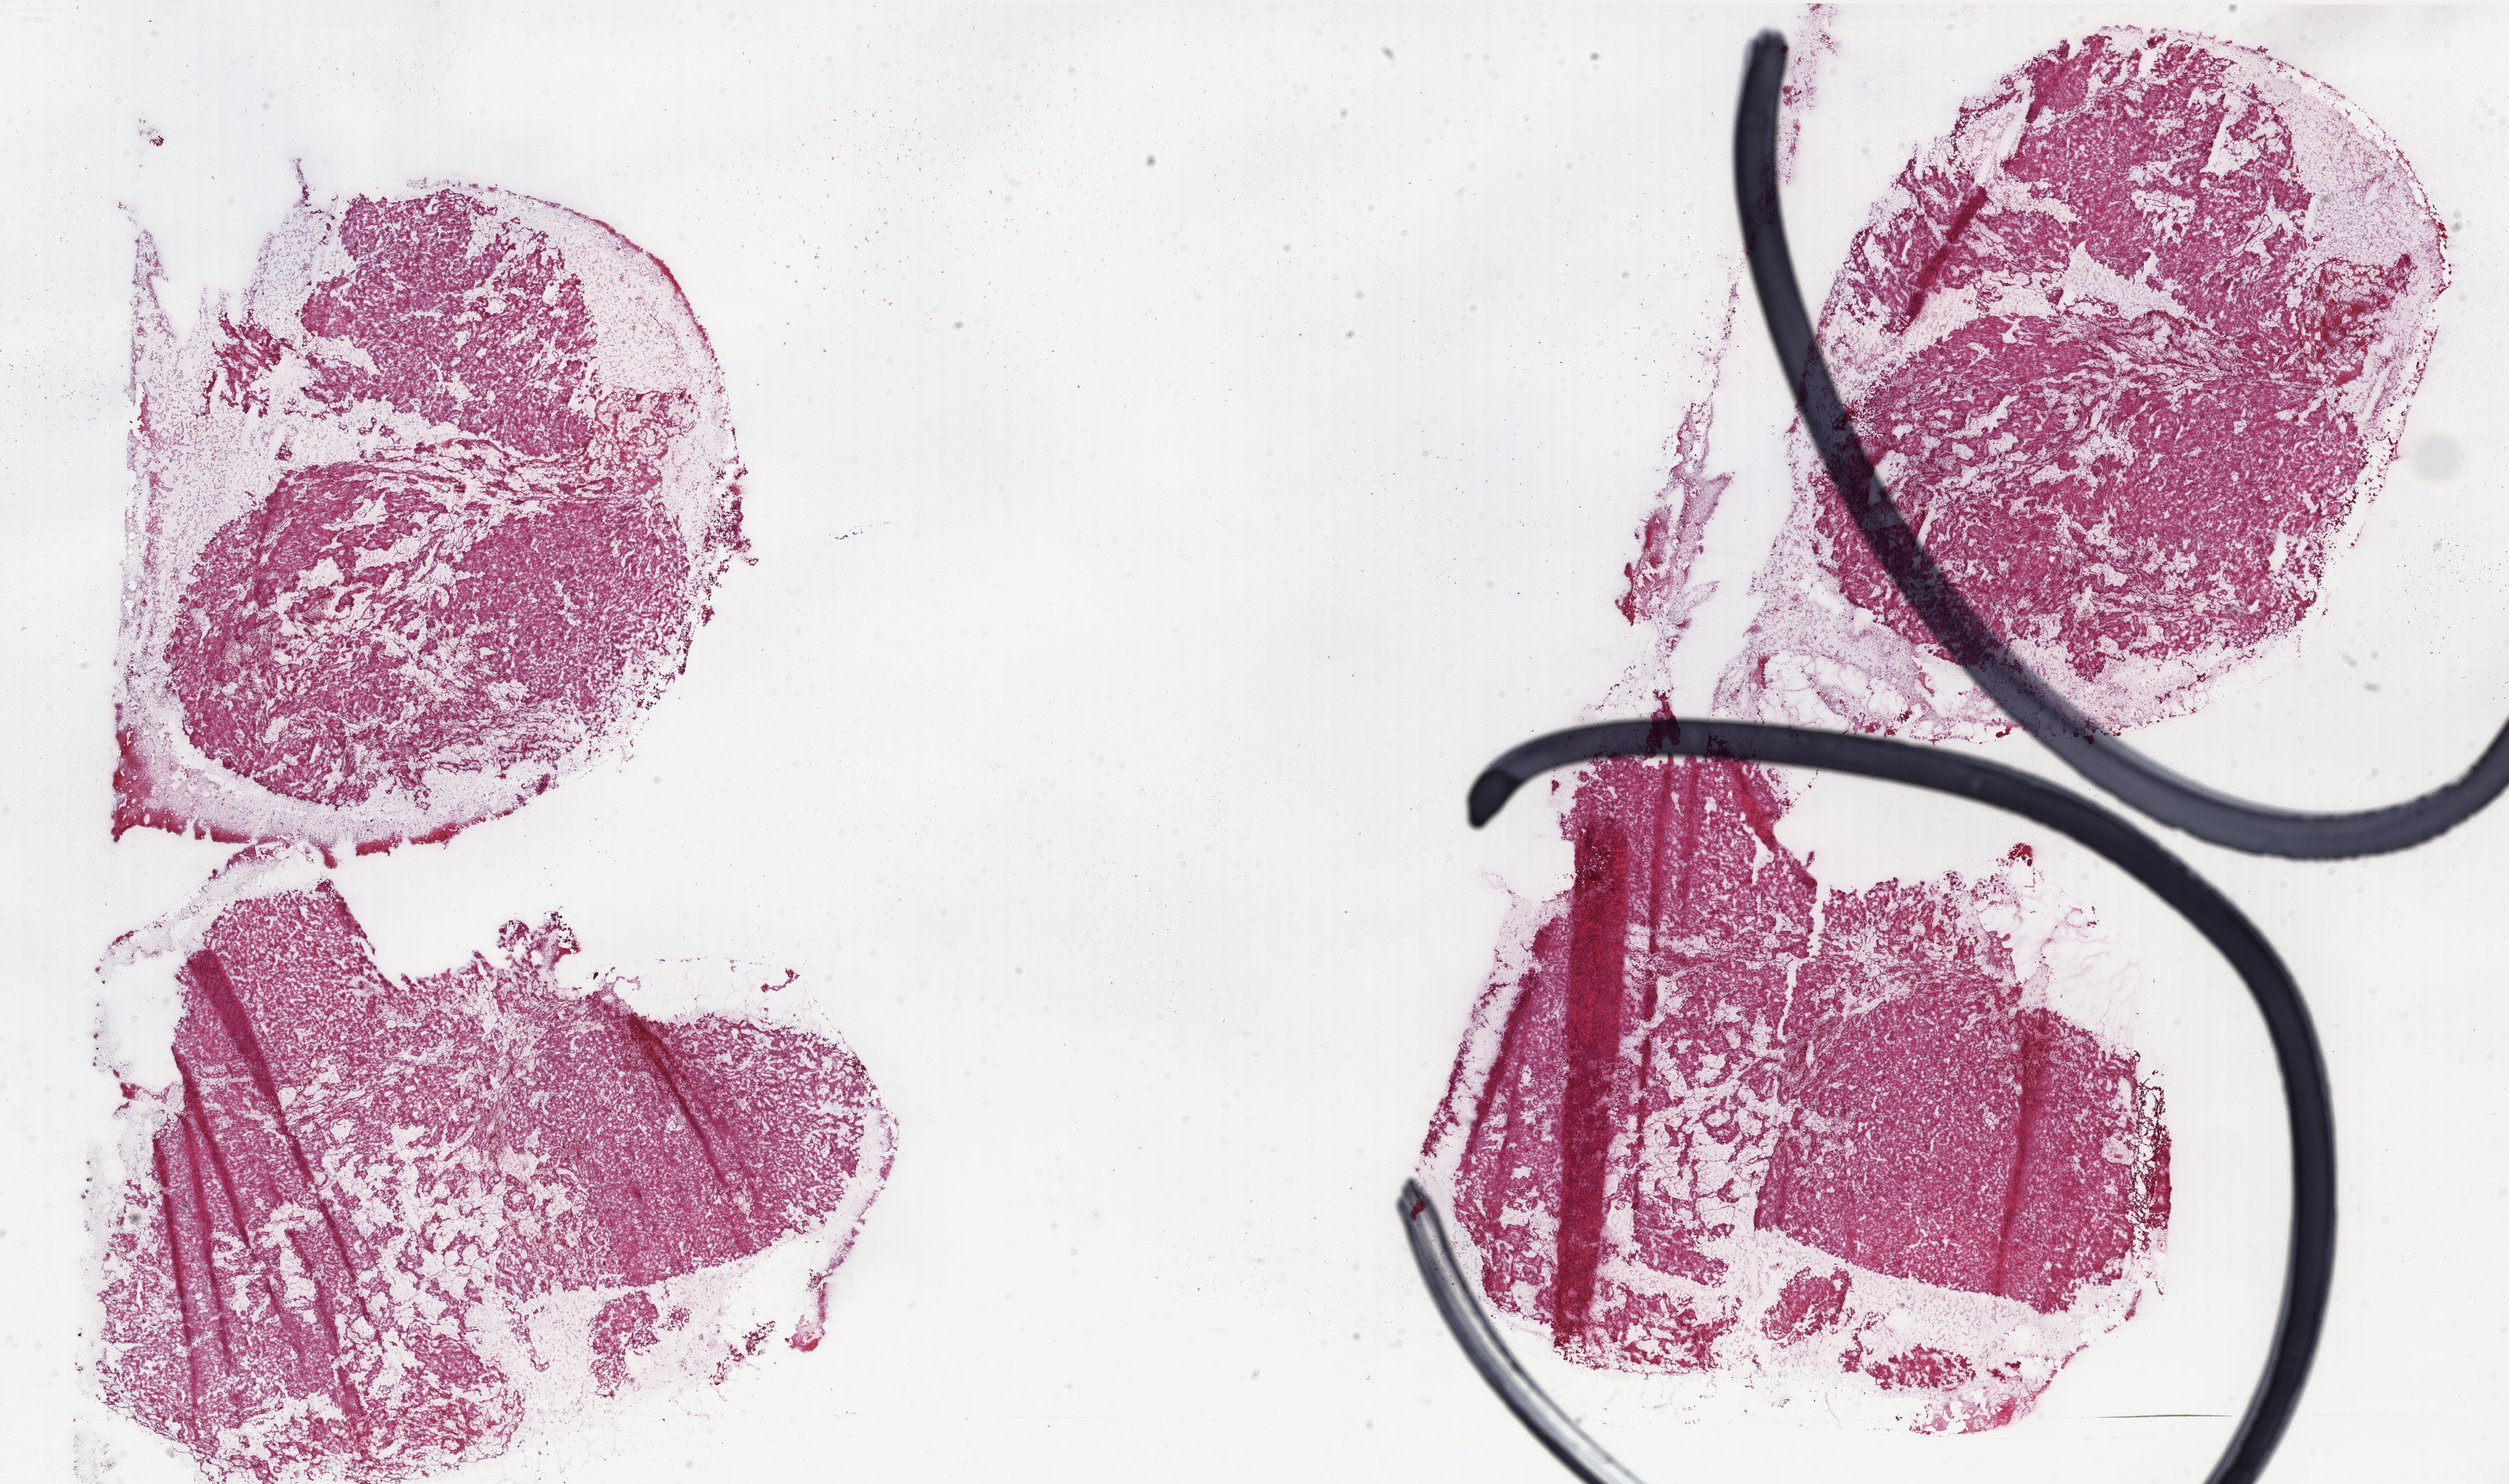
Digitized H&E-stained tissue section (whole slide) — a low-resolution overview of the entire scanned area, about 27.7 x 16.4 mm (acquisition: 40x scan). Frozen section. Kidney, primary tumour sample. Patient: female, age at initial diagnosis 51 years. Pathologist review of this section (percent, as recorded): tumour cells 100%, tumour nuclei 75%, normal cells 0%, stromal cells 0%, necrosis 0%. Inflammatory infiltration, as recorded: lymphocyte infiltration 1%, monocyte infiltration 5%, neutrophil infiltration 0%.
- histologic diagnosis: Papillary adenocarcinoma, NOS